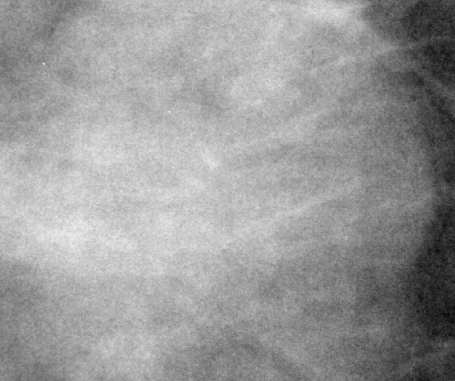
Crop from a digitized film mammogram around one marked abnormality, right breast, CC view.
- Marked abnormality: mass, shape oval, margins circumscribed / obscured; BI-RADS assessment category 3; subtlety rating 1 on a 1 (subtle) to 5 (obvious) scale; pathology (as recorded): malignant.